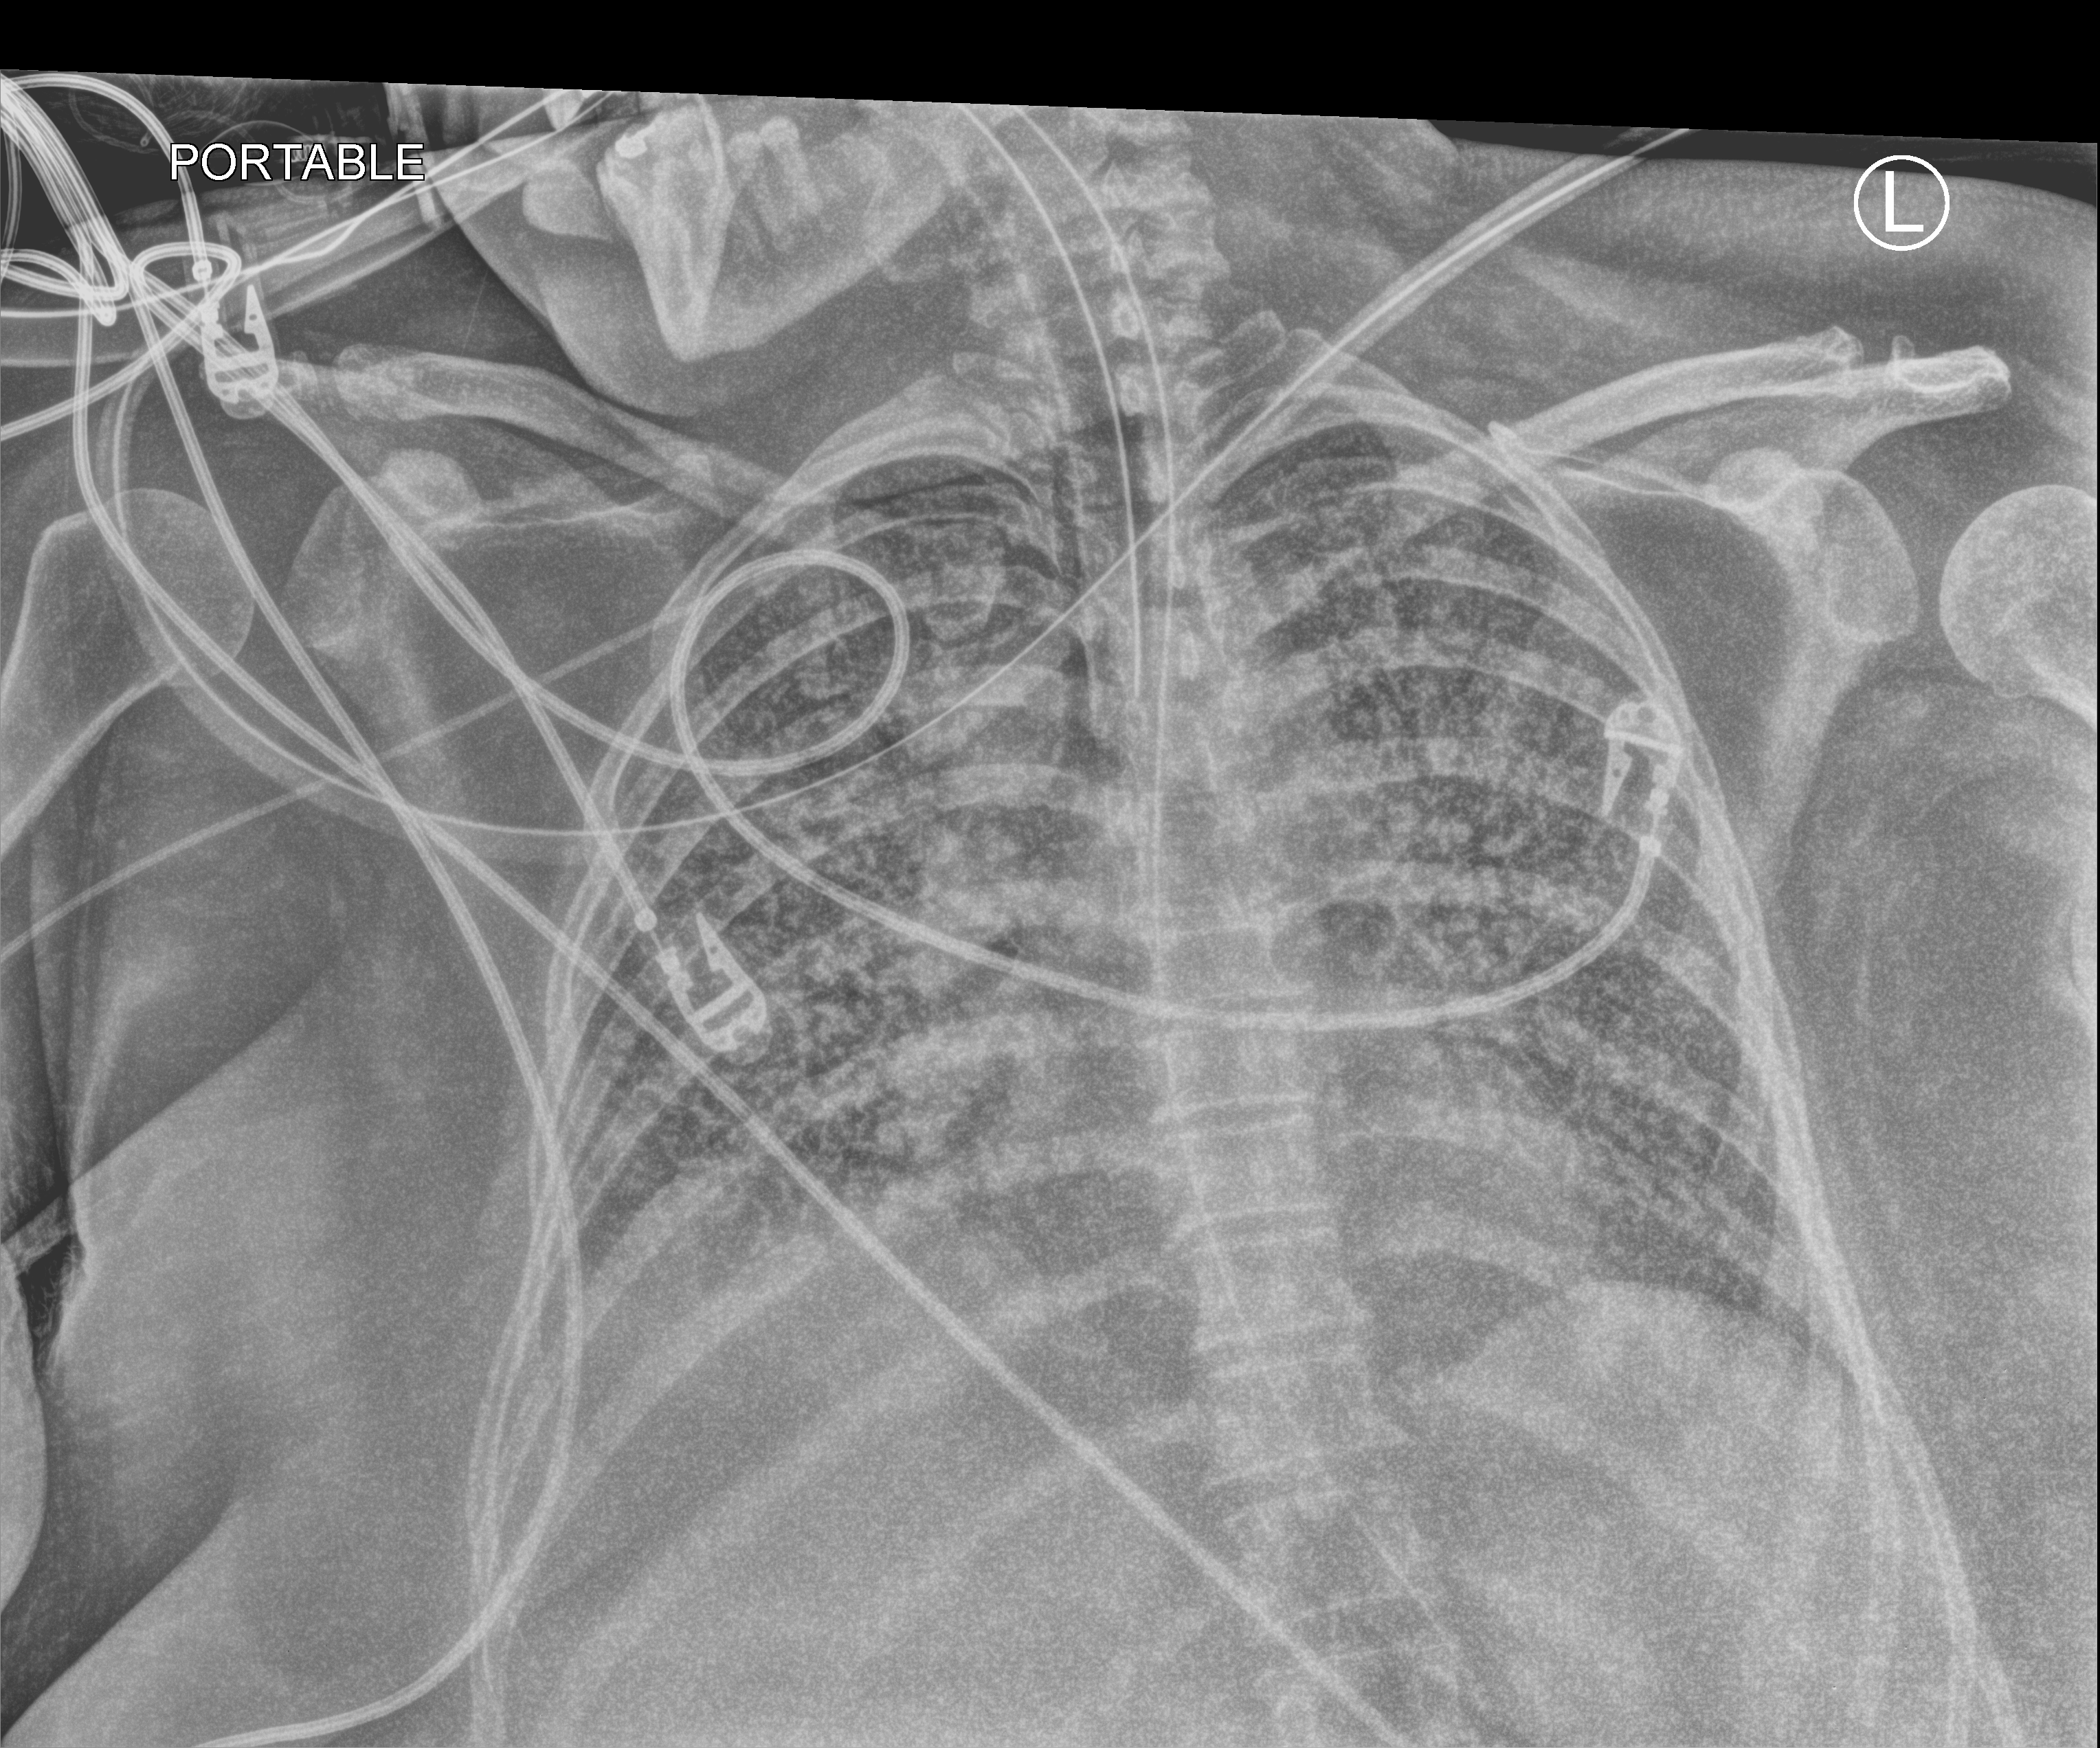
Chest X-ray (portable). Patient hospitalised with COVID-19; female, aged 18–59 years.
Hospital-stay facts (about this admission, not read from this image; timing relative to this image not recorded): other chronic lung disease (admission record): no; admitted to intensive care during this hospital stay: yes; mechanically ventilated during this hospital stay: yes.